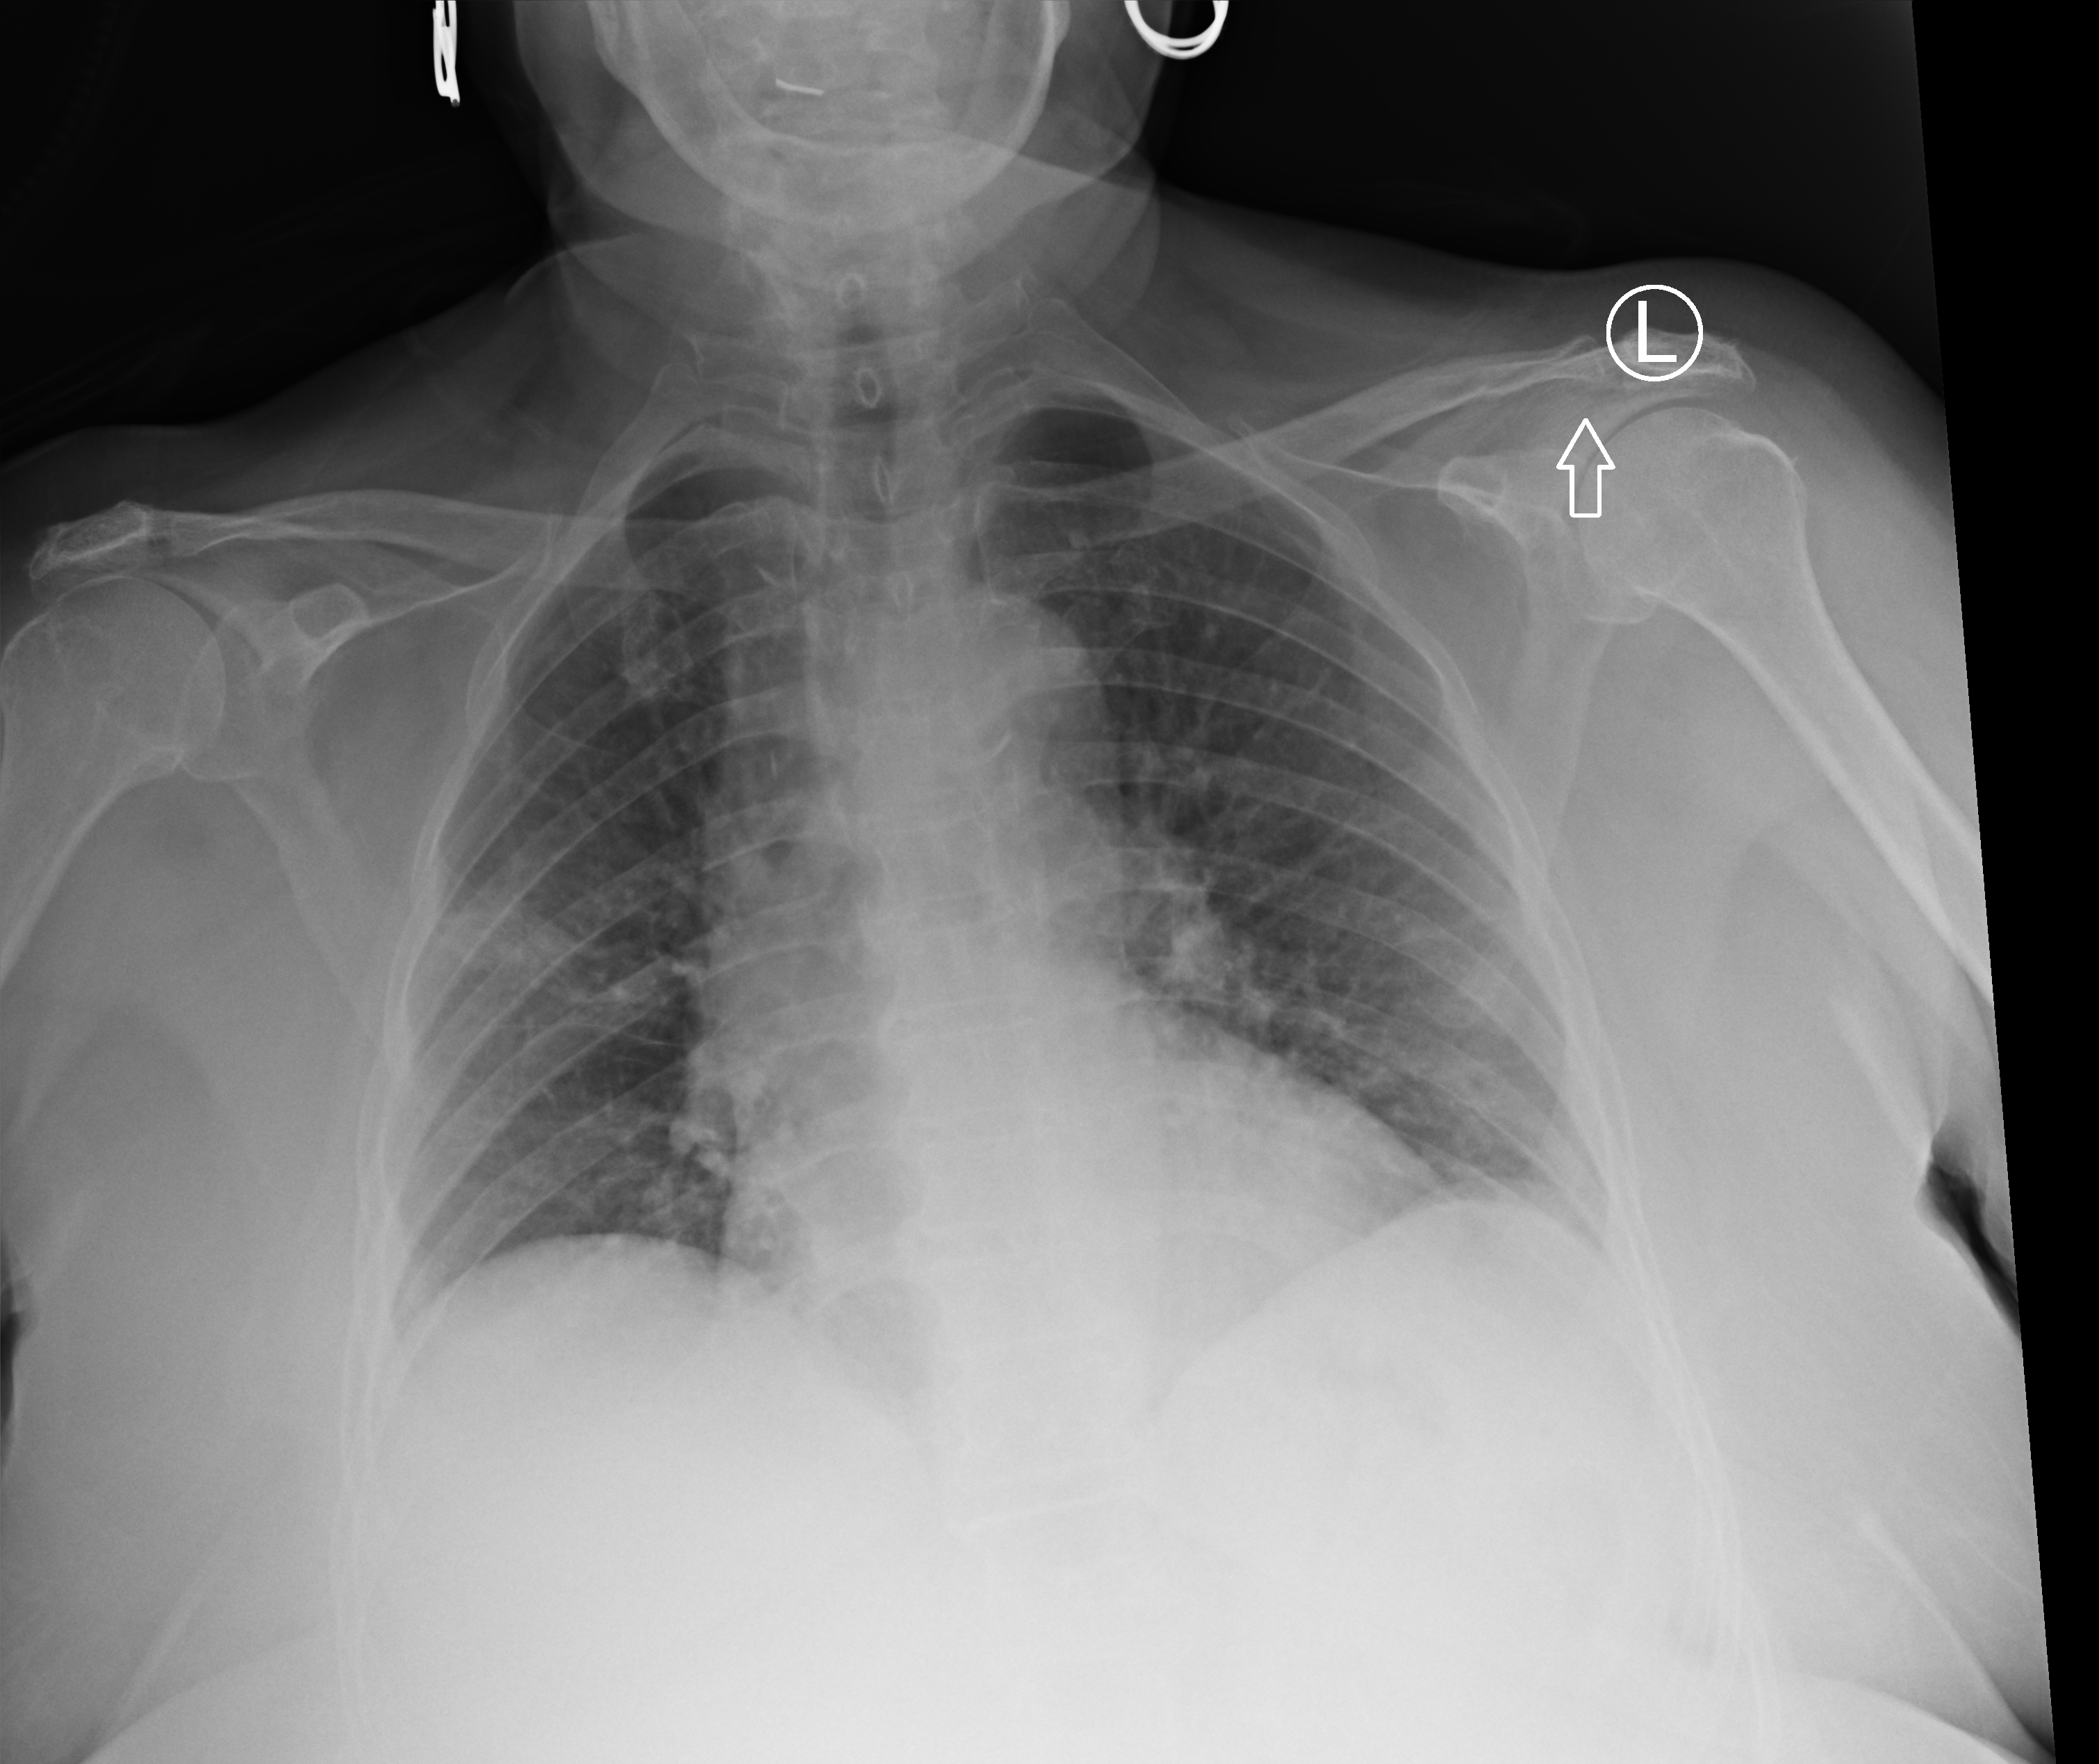
Chest X-ray (portable); anteroposterior (AP) projection. Patient hospitalised with COVID-19; female, aged 75–90 years.
From the hospital-stay record, not from the radiograph (when in the stay this image was taken is not recorded):
- length of hospital stay: 6 days
- admitted to intensive care during this hospital stay: no